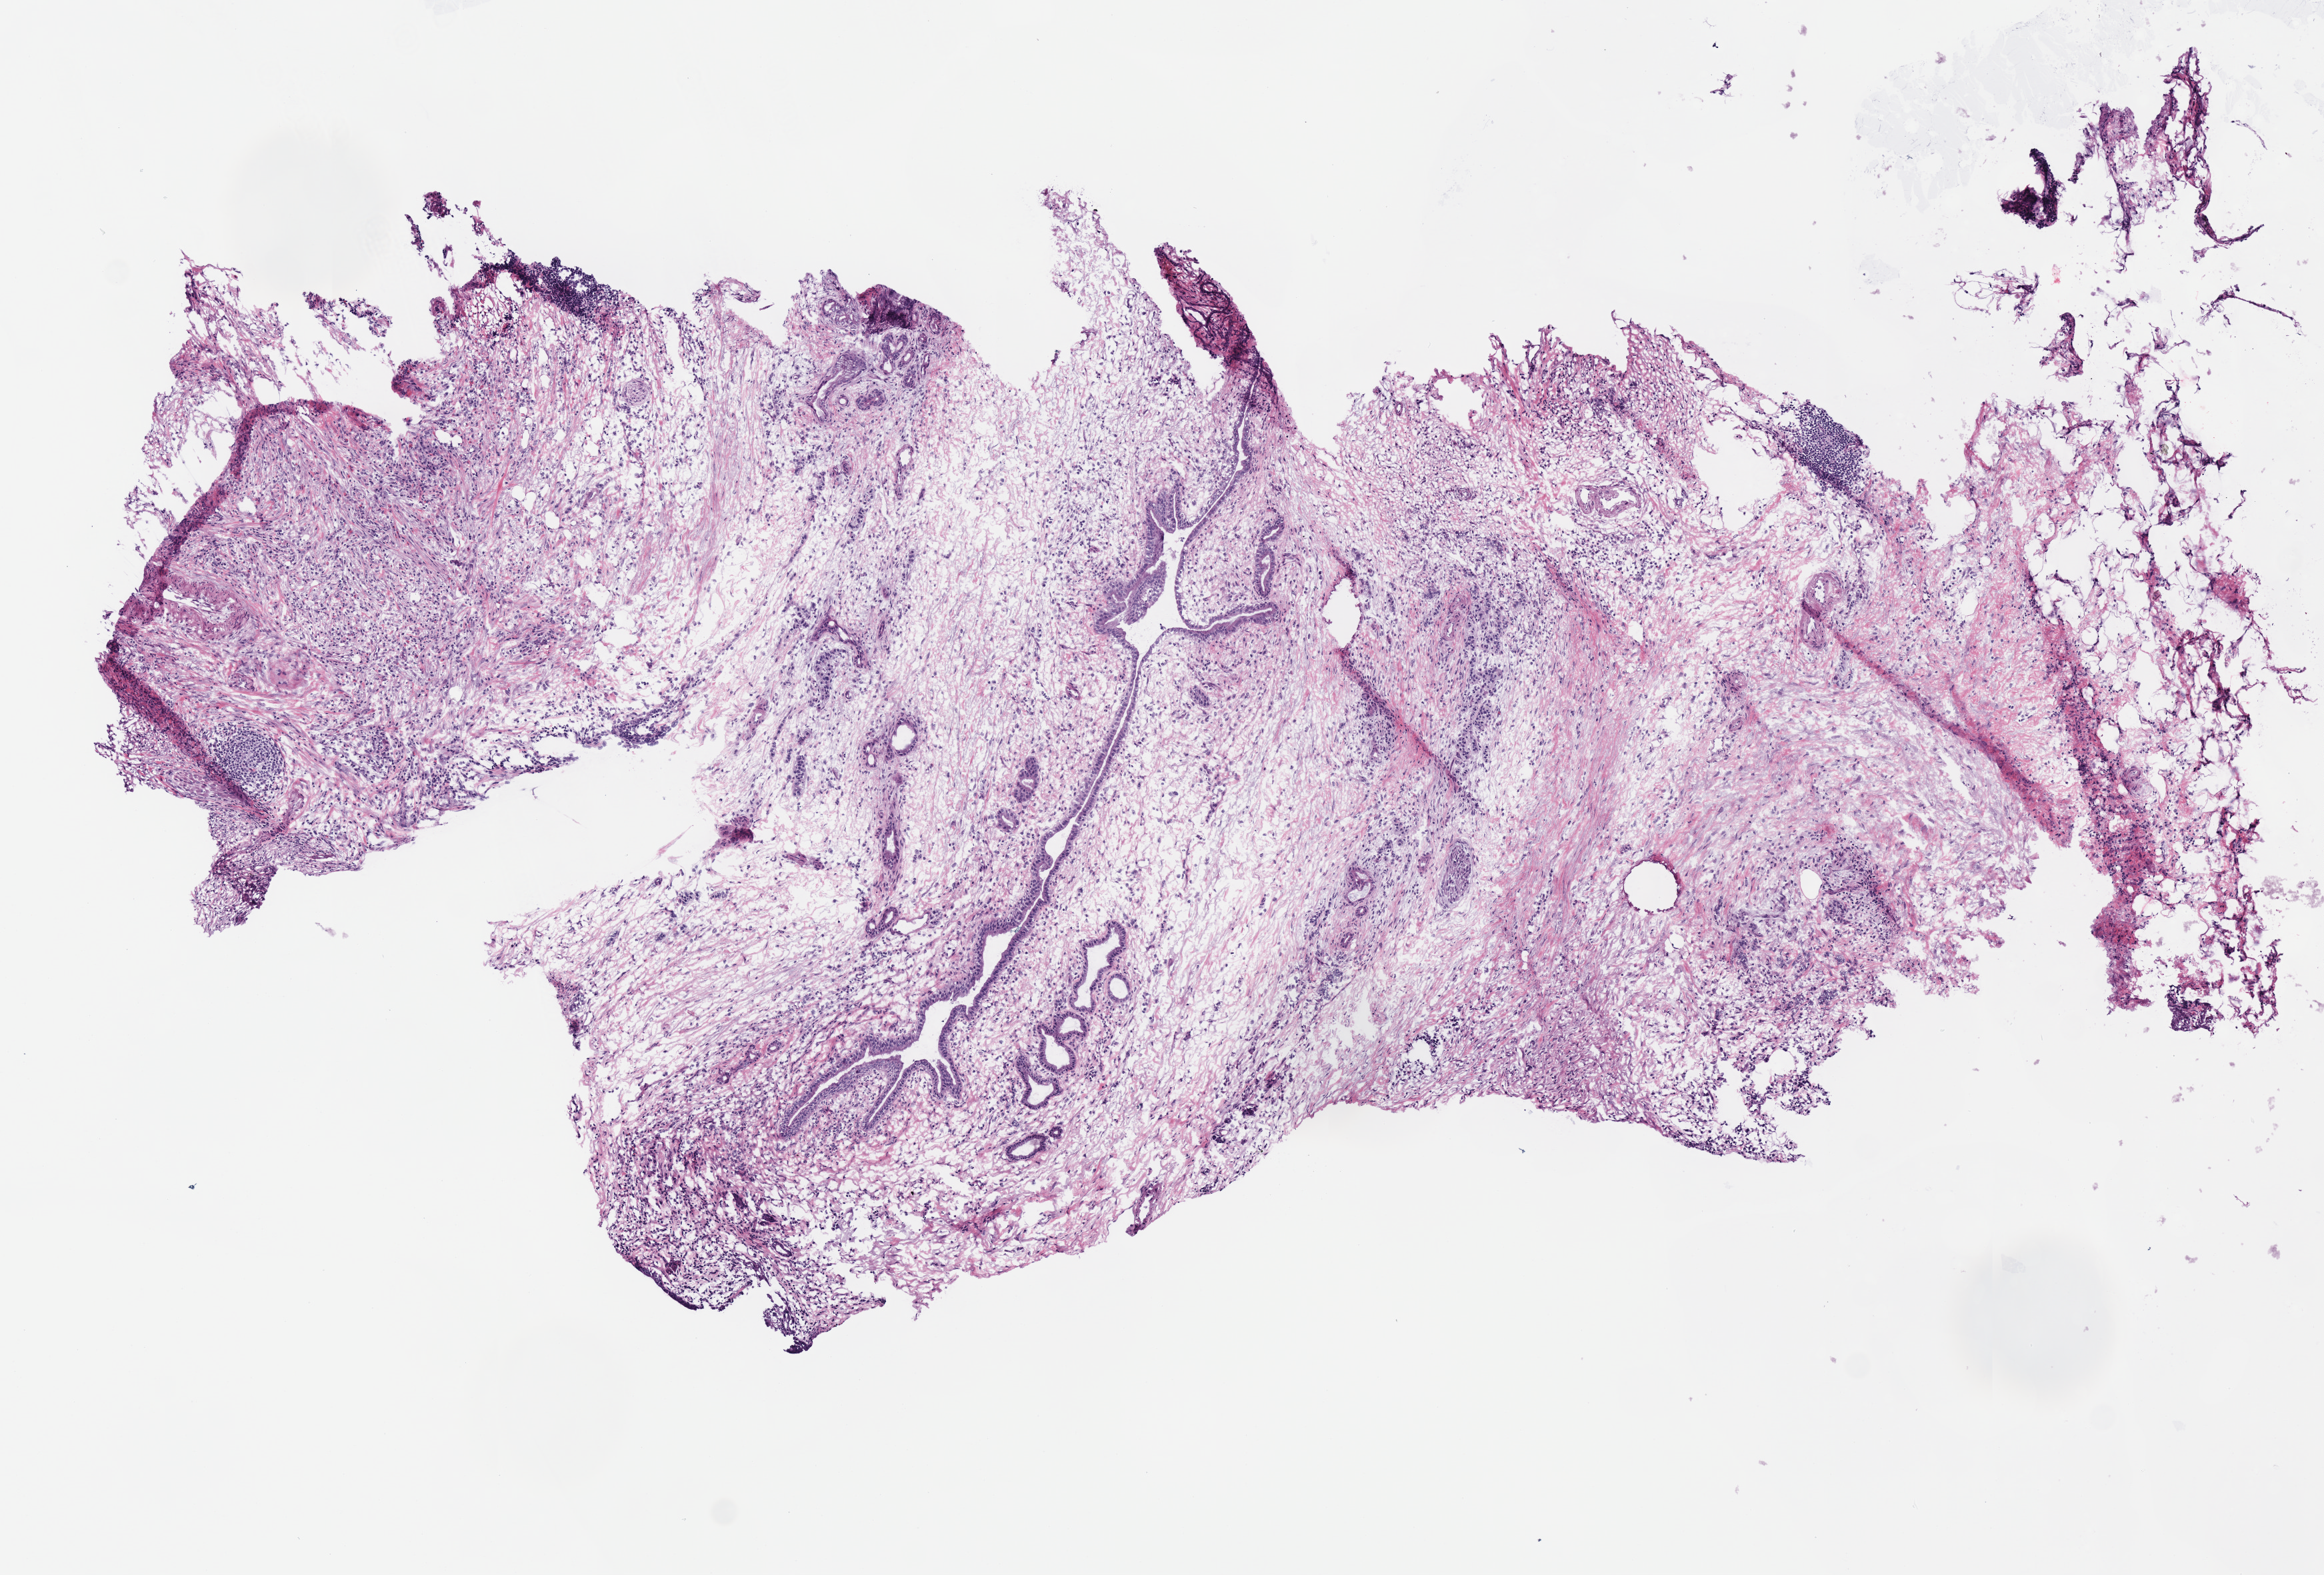
H&E whole-slide image, whole scanned area (about 6.9 x 4.6 mm) shown as a low-resolution overview, frozen section from the bottom of the tissue portion, primary tumour sample from the pancreas. Patient: male, age at initial diagnosis 65 years. Histologic grade: G2 (moderately differentiated).
• AJCC pathologic stage: IIA (7th edition)
• pathologic diagnosis: Infiltrating duct carcinoma, NOS